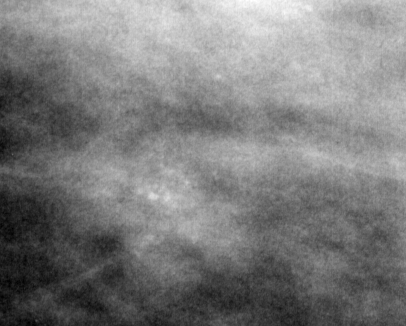
Crop from a digitized film mammogram around one marked abnormality, right breast, CC view.
Calcifications, morphology pleomorphic, distribution linear; BI-RADS assessment category 4; pathology (as recorded): malignant.